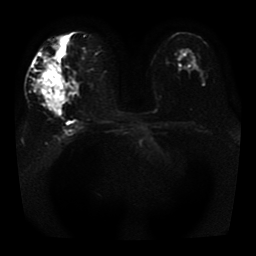
Breast MRI, one axial slice. Slice 22 of 41 in the series (ordered by position). Diffusion-weighted series; image 2 of 4 stored at this slice position (different b-values; order by instance number). 1.5 T. 256 × 256 image matrix, field of view 330 × 330 mm. Female patient.
Annotated regions visible in this slice (manually delineated by an expert):
- tumour on diffusion-weighted imaging: bounding box [x1, y1, x2, y2] px = [36, 65, 66, 108]